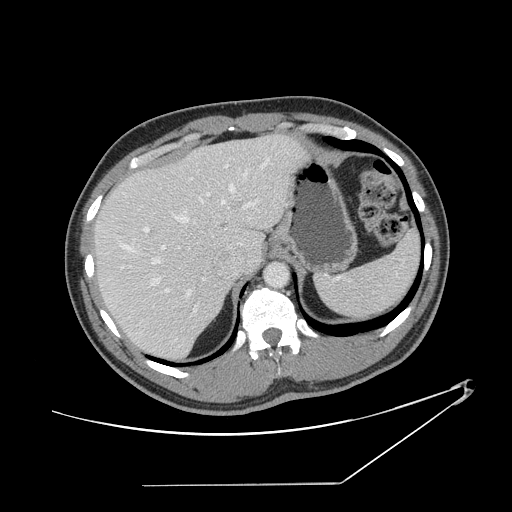
Contrast-enhanced abdominal CT, one axial slice; position 108 of 152 along the scan axis; reconstruction kernel STANDARD; 120 kVp; intravenous contrast given; soft-tissue window (W 400 / L 40 HU); 2.5 mm slice thickness; 512 × 512 image matrix. Male patient, age 45 years. Case-level facts recorded for this patient, not image findings: diagnosis: colorectal cancer liver metastases, imaged before liver resection; multiple liver metastases: no; largest metastasis: 1 cm.
Annotated regions visible in this slice (manually delineated by an expert):
- hepatic veins: bounding box <111,158,270,298> (left, top, right, bottom; pixels)
- liver: <96,135,301,361>
- planned liver remnant (the part of the liver to remain after resection): <96,155,234,361>
- portal vein (with intrahepatic branches): <161,193,255,314>